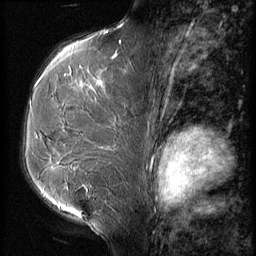
Breast MRI (dynamic contrast-enhanced), one sagittal slice. Slice 36 of 56 in the series (ordered by position). 3 images stored at this slice position (order not interpretable as contrast timing). 1.5 T. TE 4.2 ms, TR 9 ms. 2.5 mm slice thickness. 256 × 256 image matrix, field of view 180 × 180 mm. Female patient, age 51 years. From the clinical record (not read from this slice): setting: breast cancer imaged before/during neoadjuvant chemotherapy; receptor status: HR-positive, HER2-negative.
Annotated regions visible in this slice (semi-automatically segmented with operator editing):
- analysis volume of interest (the breast-tissue region the enhancement analysis was run in; not a lesion): bounding box [x1, y1, x2, y2] px = [23, 56, 145, 165]
- tumour enhancement mask (voxels above the 140 % enhancement threshold inside the analysis volume of interest): [35, 70, 102, 89]